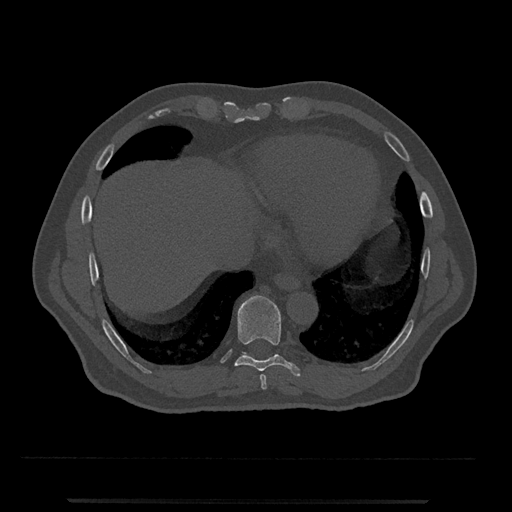
CT including the spine, one axial slice. Position 569 of 797 along the scan axis. Bone window (W 1800 / L 400 HU). 0.5 mm slice thickness. 512 × 512 image matrix, field of view 419 × 419 mm. Male patient, age 63 years. From the clinical record (not read from this slice): primary cancer: prostate.
Outlined on this slice (semi-automatically segmented with operator editing):
- T10 vertebra: bounding box (x1, y1, x2, y2) in pixels: (242, 352, 247, 354)
- T8 vertebra: (260, 374, 267, 390)
- T9 vertebra: (235, 295, 301, 377)